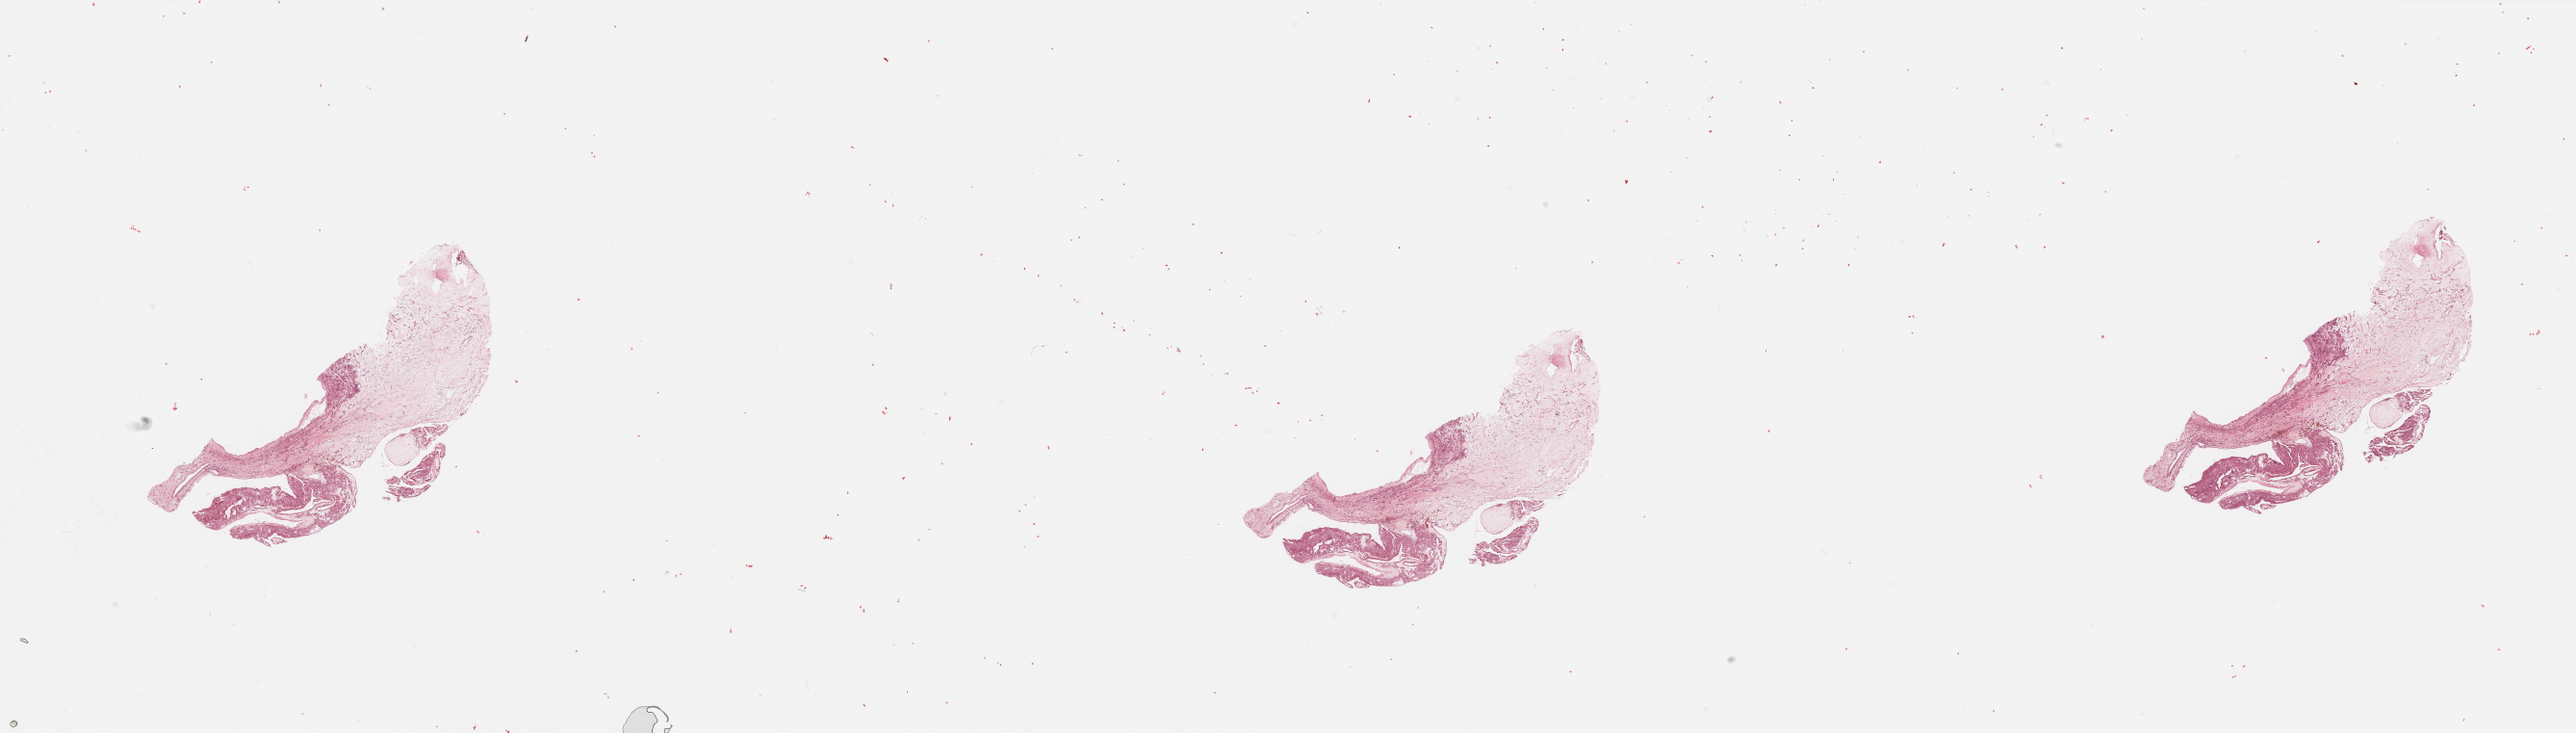
H&E whole-slide image, shown as a low-resolution overview of the whole scanned area (about 42.3 x 12.0 mm); tumour tissue sample, kidney. Patient: male, age 63 years. Histologic grade: G2 (moderately differentiated).
- histologic diagnosis: Renal cell carcinoma, NOS
- AJCC pathologic stage: III
- primary tumour site (as recorded): upper pole